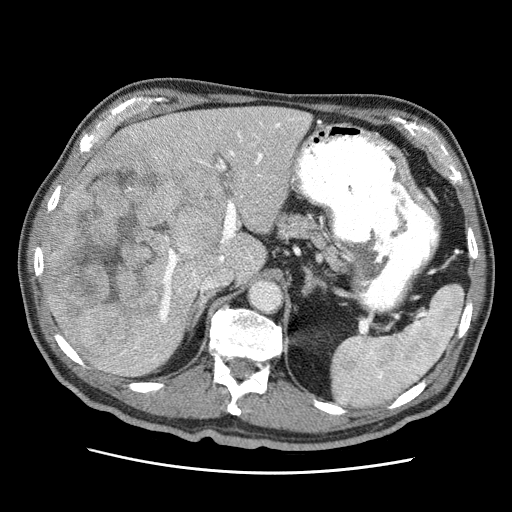
Contrast-enhanced abdominal CT (liver protocol), one axial slice; slice 33 of 75 in the series (ordered by position); 120 kVp; soft-tissue window (W 400 / L 40 HU); 2.5 mm slice thickness; 512 × 512 image matrix. Case-level facts recorded for this patient, not image findings: diagnosis: hepatocellular carcinoma (patient treated with transarterial chemoembolisation; whether this scan precedes or follows treatment is not stated here); TNM stage (as recorded): Stage-IIIA; Child-Pugh class: A; tumour size: 13.9 cm.
Structures marked on this image (semi-automatic segmentation, software-assisted and operator-edited):
- liver parenchyma outside the tumour (the mass and vessels are separate outlines, so this box may not span the whole liver): bounding box (x1, y1, x2, y2) in pixels: (39, 106, 310, 376)
- mass: (48, 135, 226, 359)
- liver vessels: (120, 117, 307, 361)